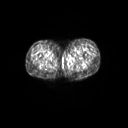
FDG PET of an extremity soft-tissue mass (from a PET/CT study), one axial slice. 3.27 mm slice thickness. 128 × 128 image matrix. Female patient, age 24 years. From the clinical record (not read from this slice): histological type: leiomyosarcoma; grade: high; site of the primary tumour: groin.
Outlined on this slice (expert contour drawn on MRI and transferred to this co-registered scan by the dataset authors):
- gross tumour volume including surrounding oedema: bounding box <62,59,69,62> (left, top, right, bottom; pixels)